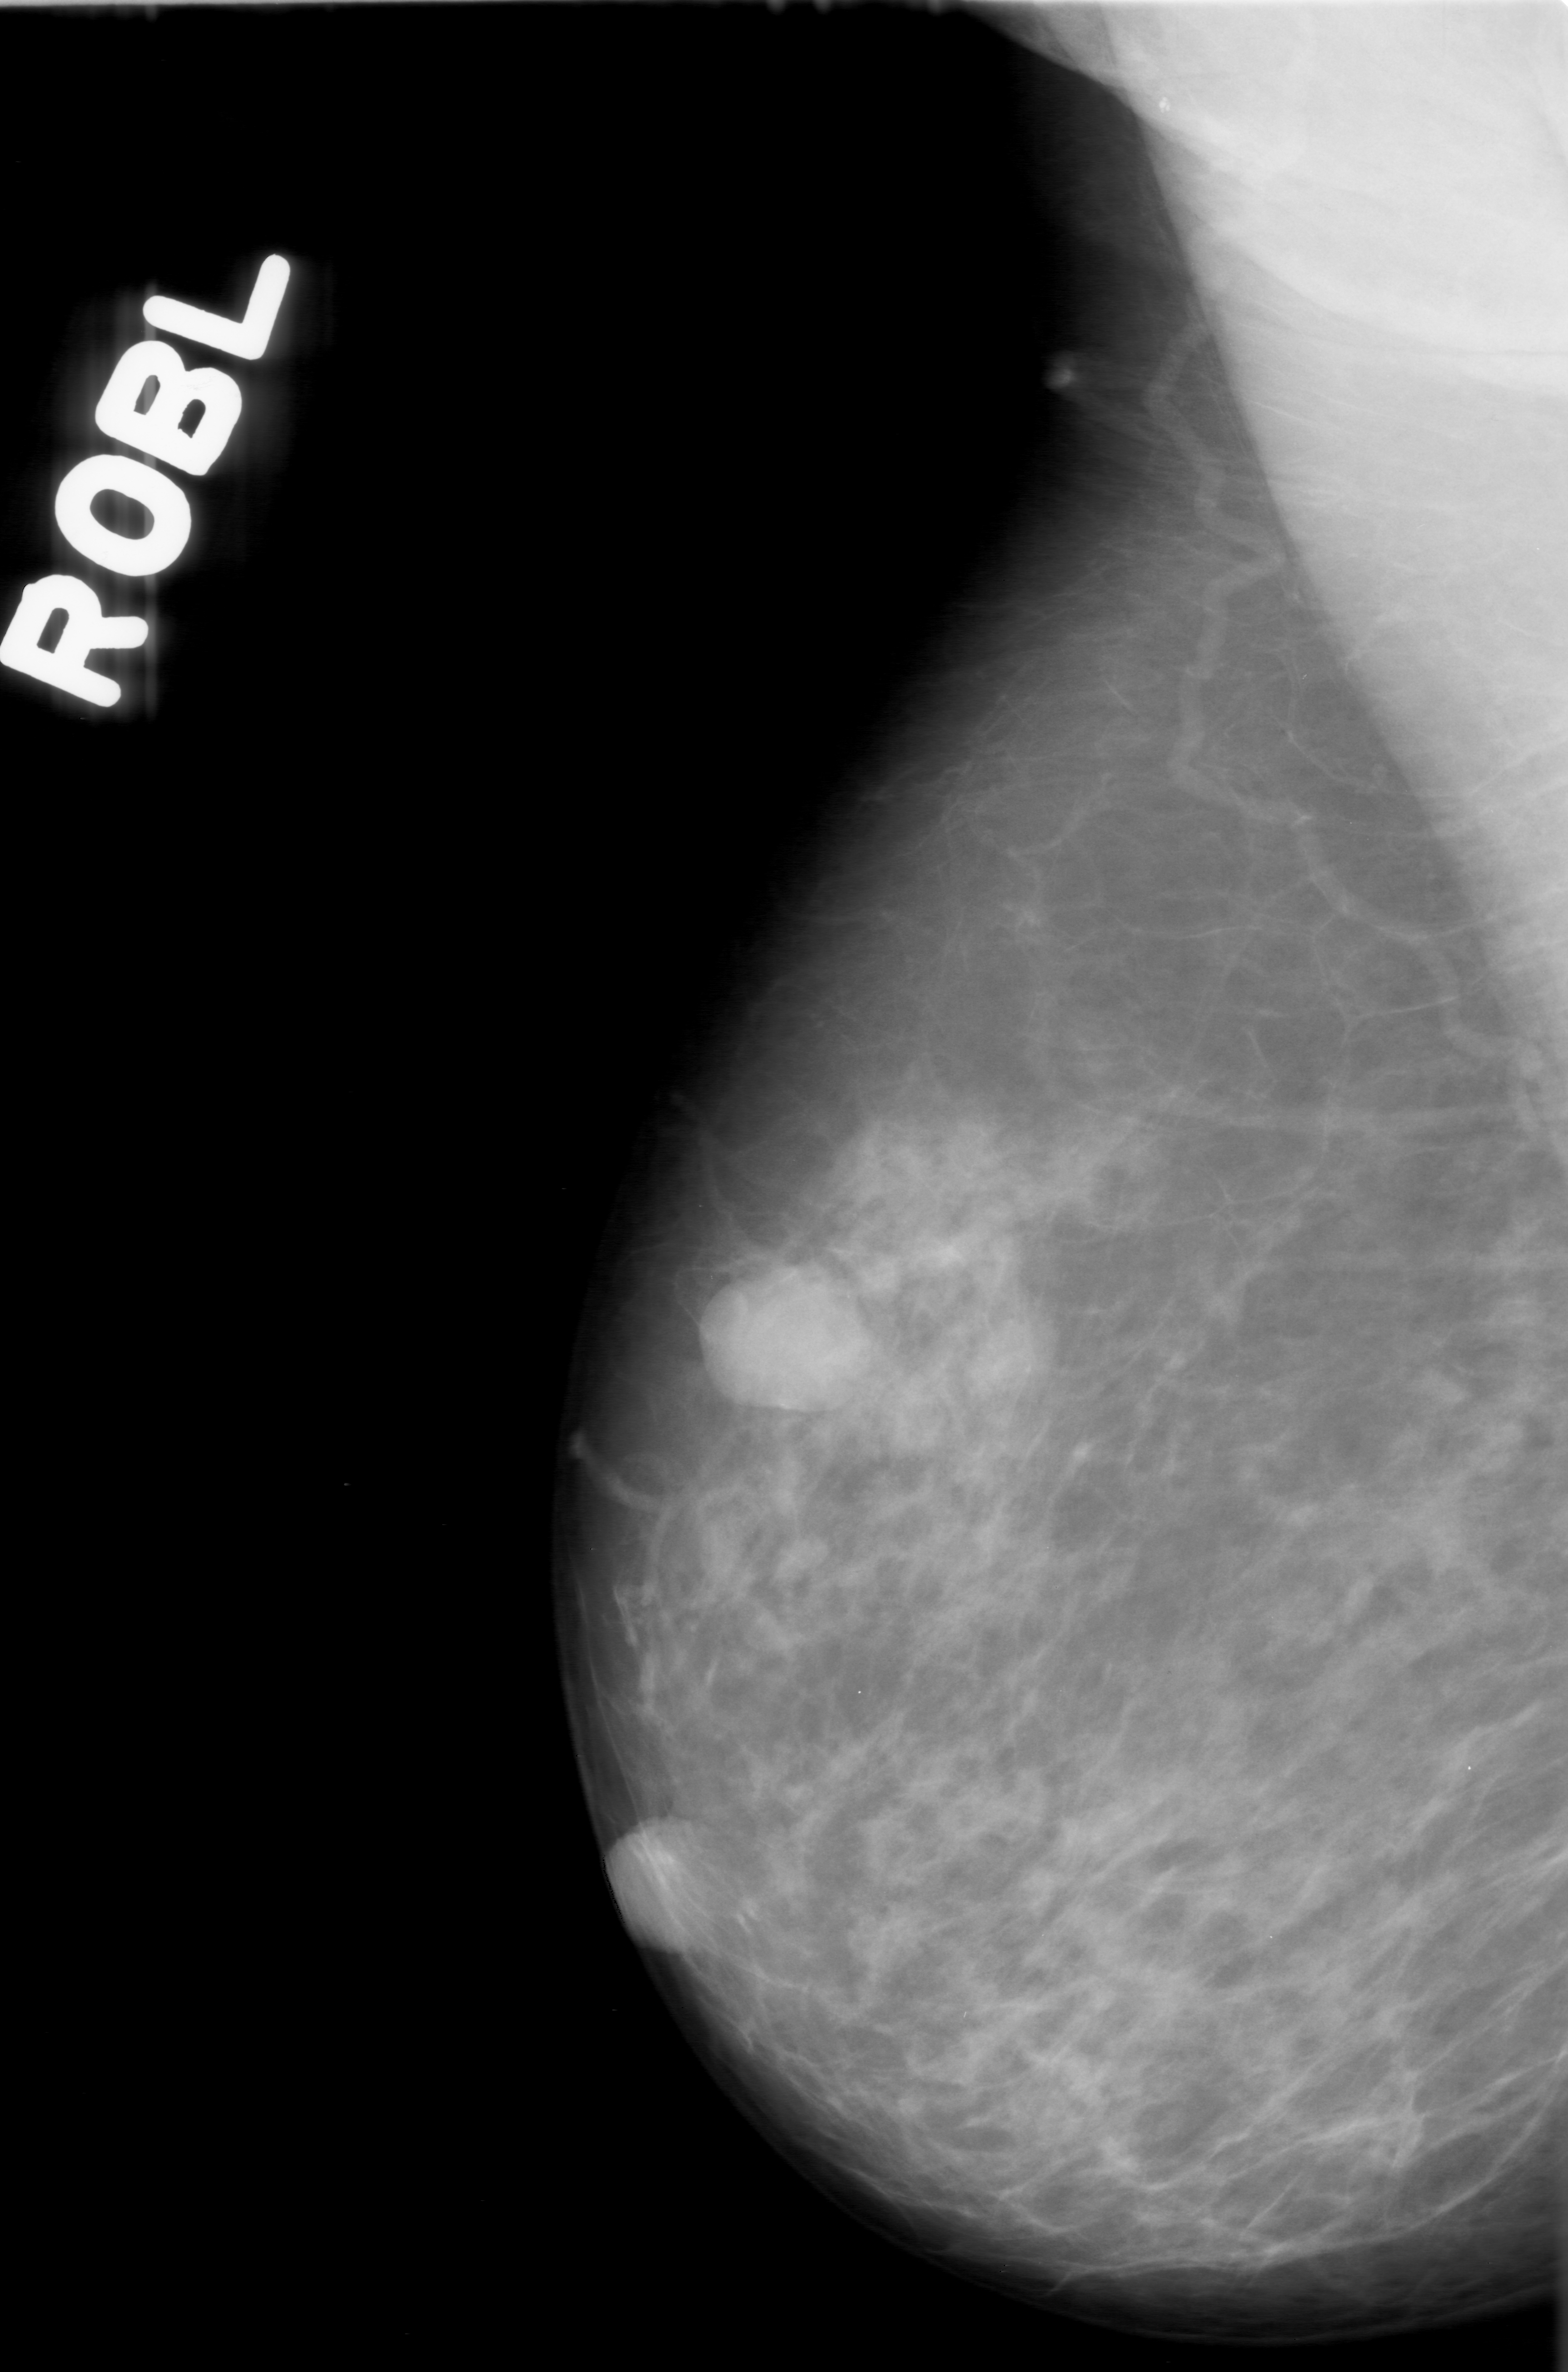
Mammogram (digitized film); right breast; mediolateral oblique (MLO) view; breast composition: scattered fibroglandular densities (BI-RADS density category 2 of 4).
Mass, shape round, margins spiculated; BI-RADS assessment category 3; pathology result (as recorded, not read from the image): malignant.